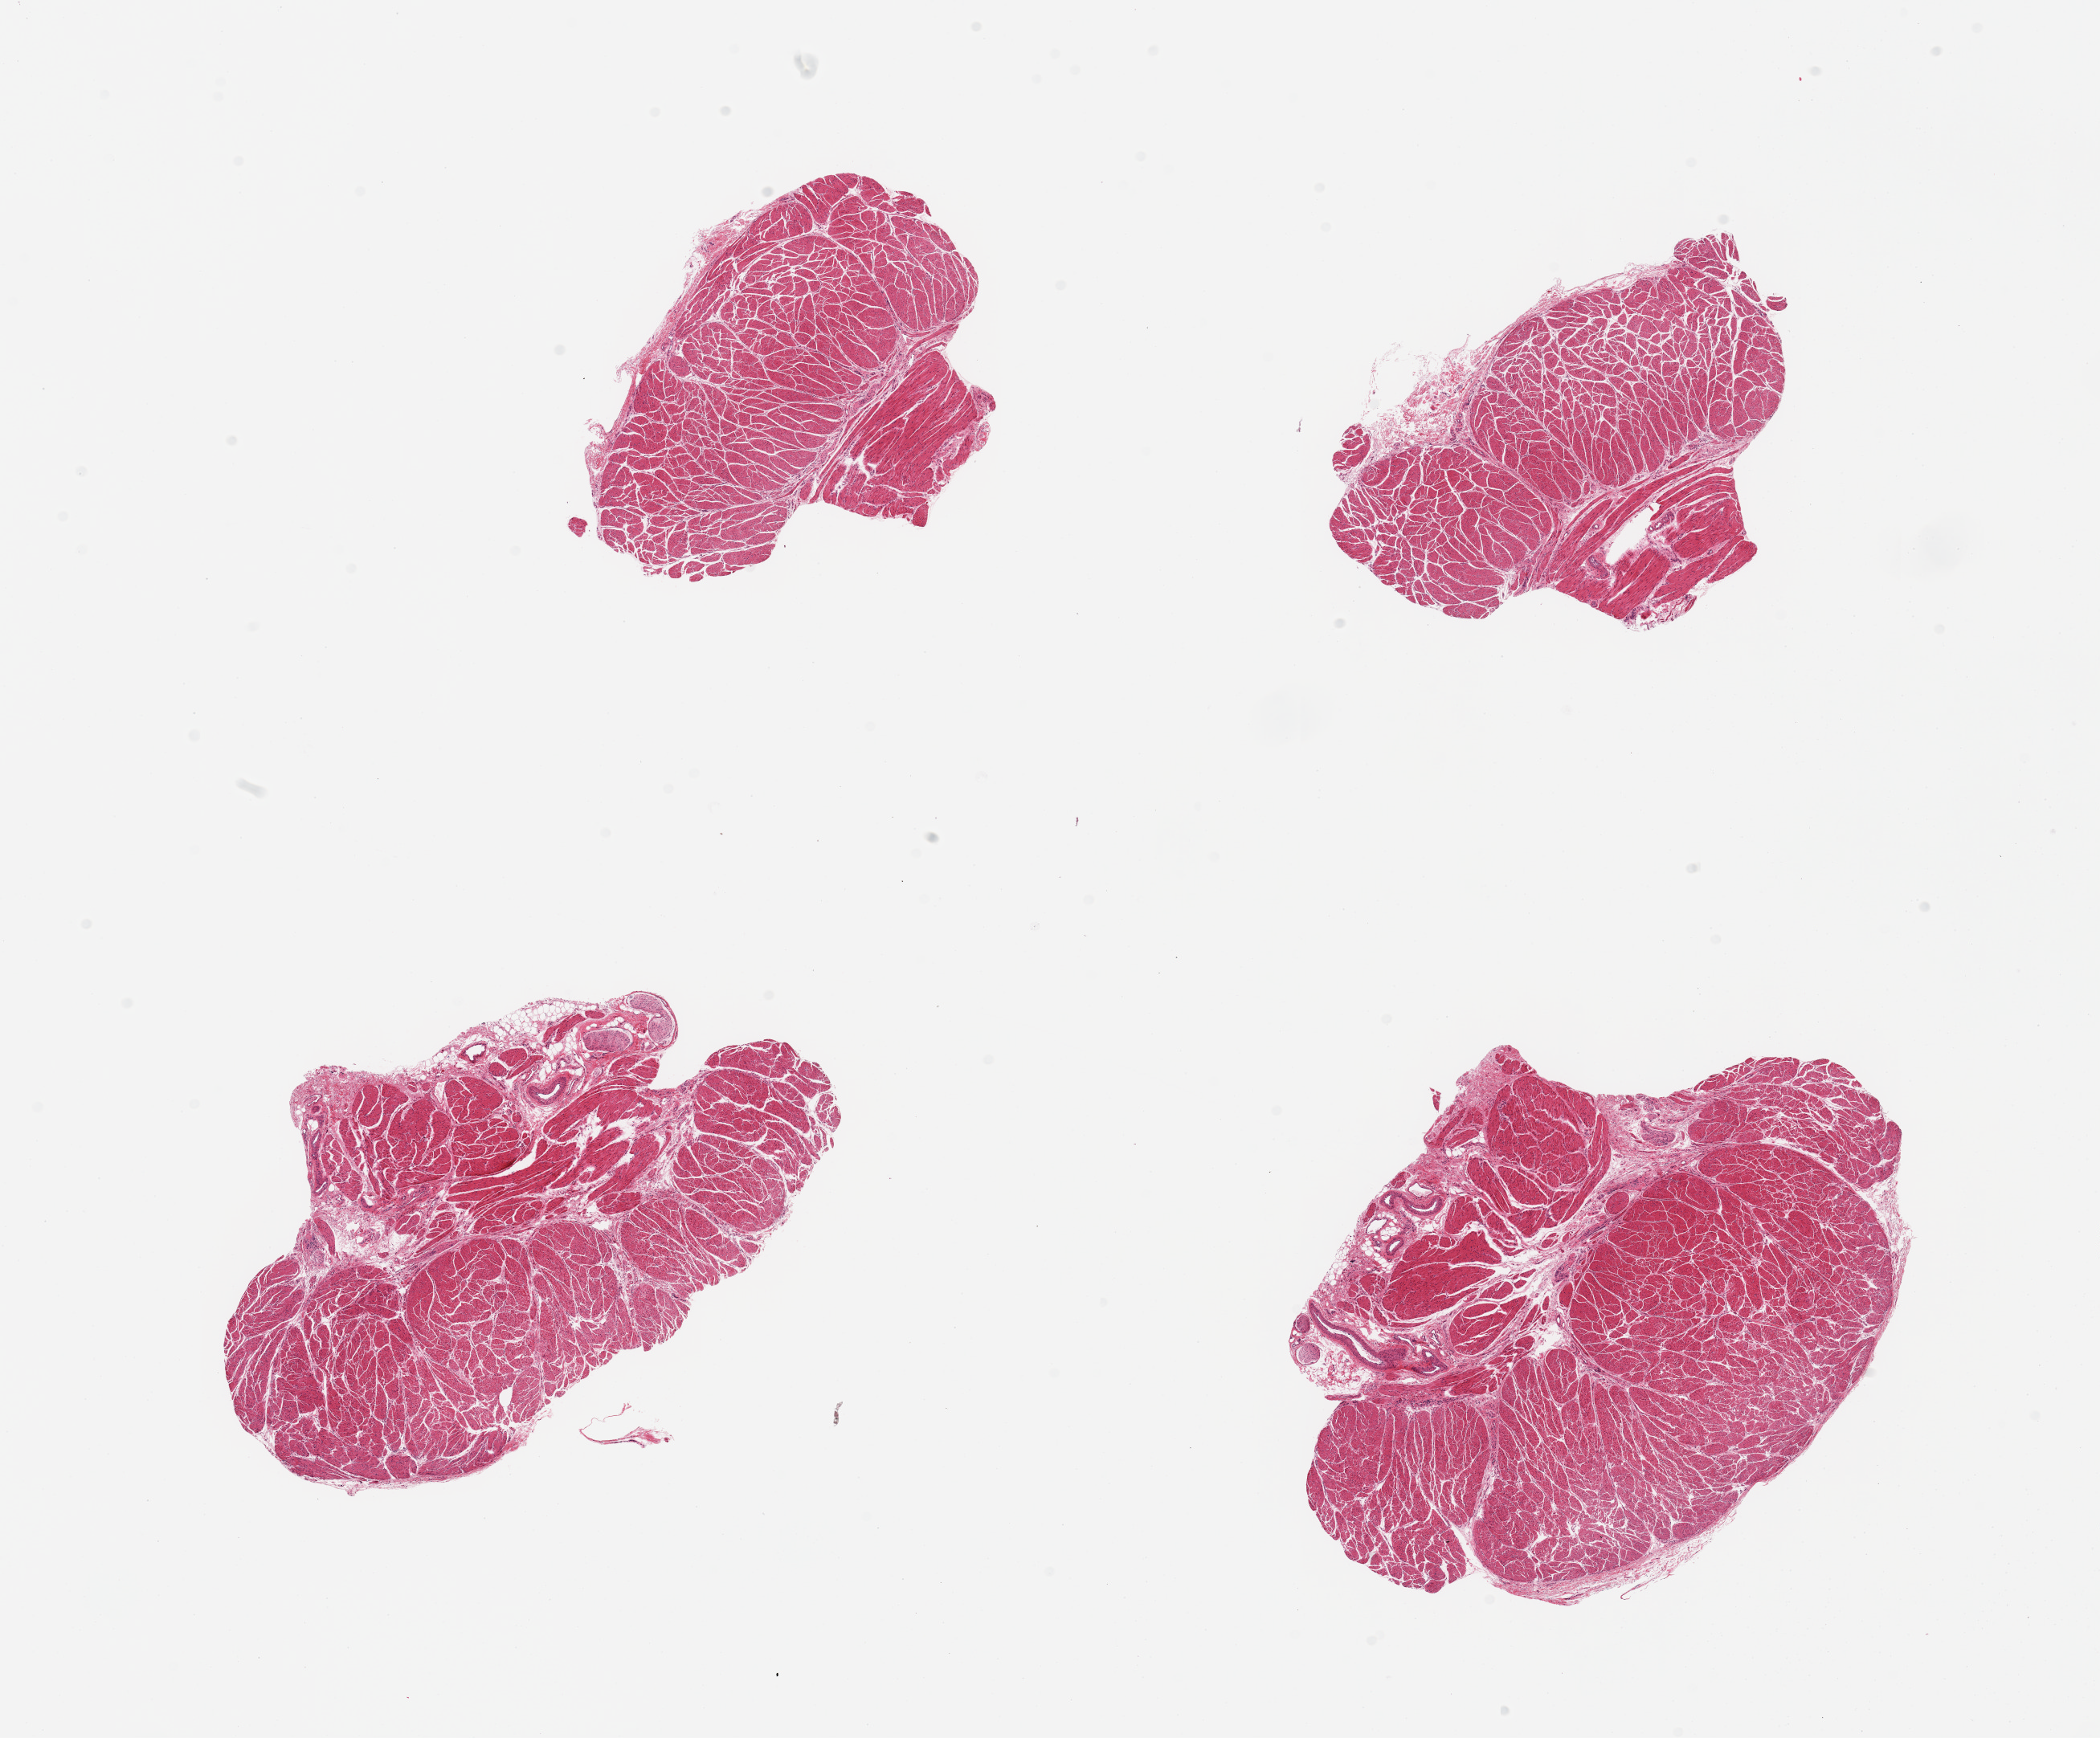
Whole-slide image, haematoxylin and eosin stain — low-resolution overview of the scanned area, about 20.7 x 17.1 mm (from a 20x scan), PAXgene-fixed paraffin-embedded (PFPE) section, section of esophageal muscle (target tissue), tissue donor sample.
* review note (as recorded): 4 pieces; well trimmed, 2 include significant nerve and vessels